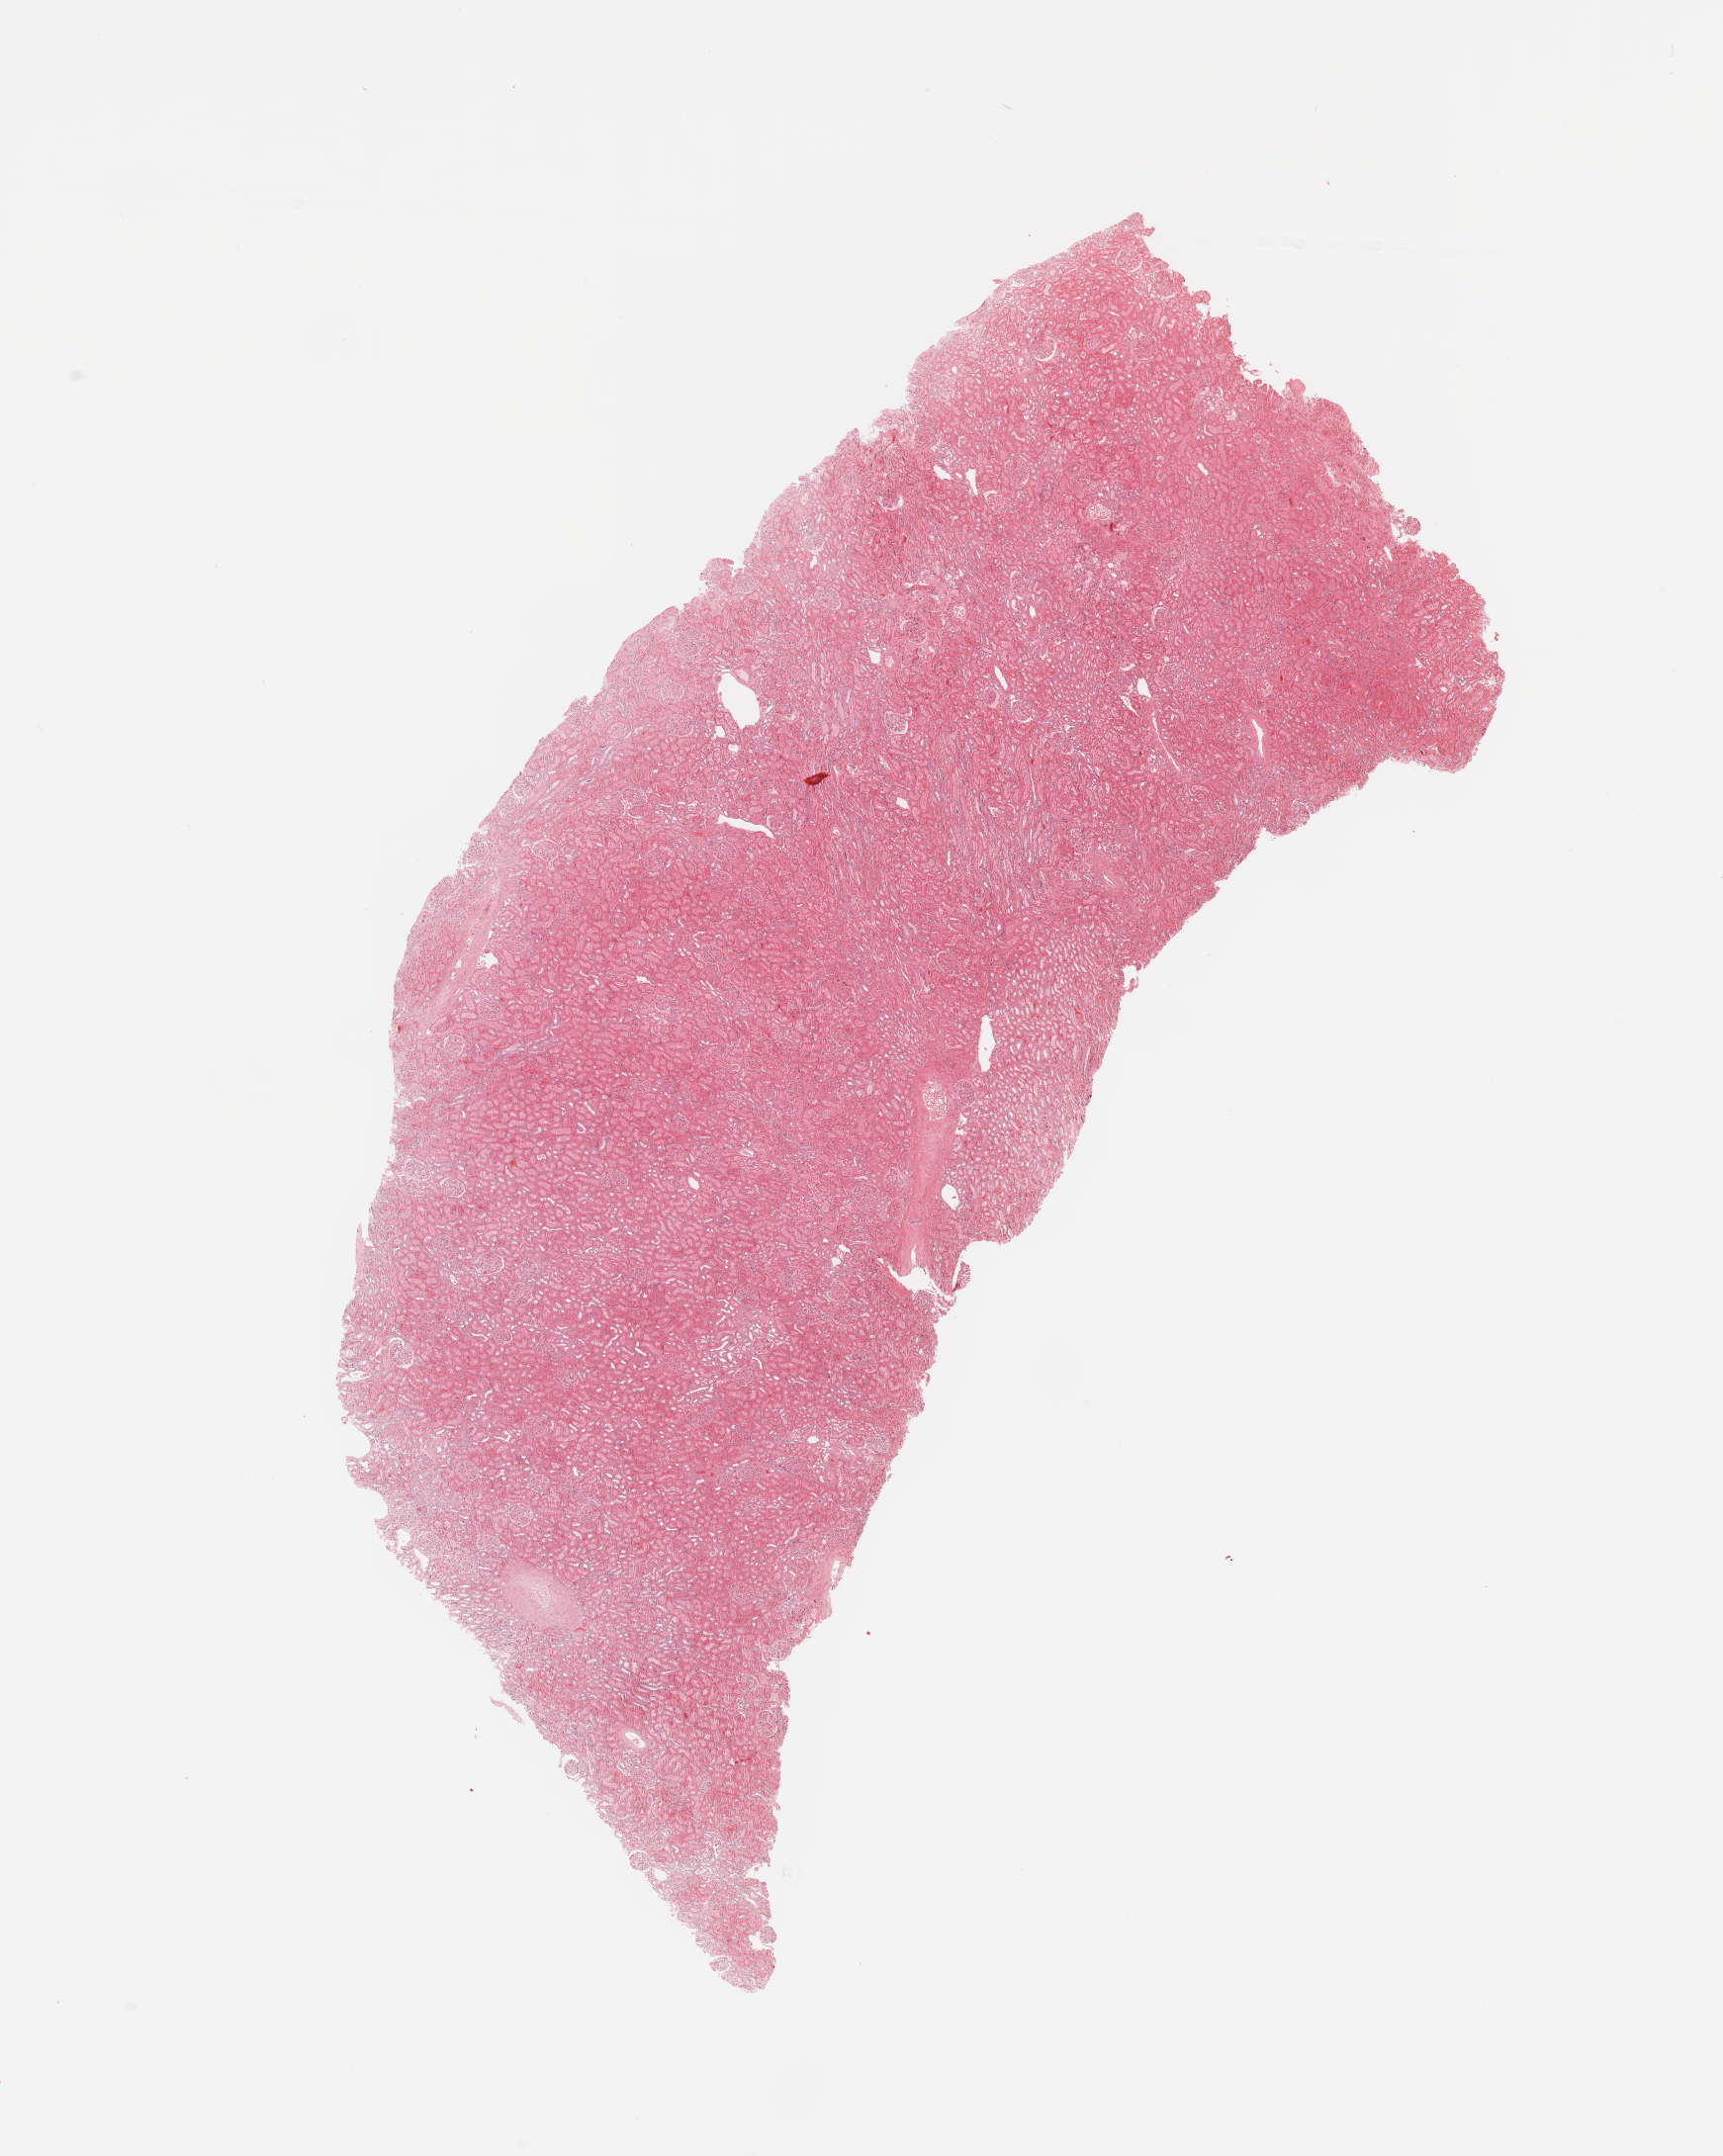
Whole-slide histology image, H&E — shown as a low-resolution overview of the whole scanned area (about 13.8 x 17.2 mm), kidney, normal (non-tumour) tissue. Male, 50 y/o.
* this section: normal (non-tumour) tissue from the same patient
* patient diagnosis: Renal cell carcinoma, NOS